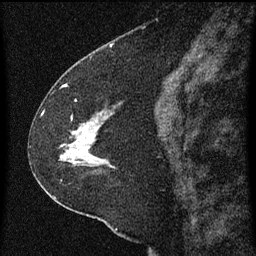
Breast MRI (dynamic contrast-enhanced), one sagittal slice; slice 31 of 60 in the series (ordered by position); dynamic contrast-enhanced series, image 2 of 3 at this slice position (ordered by acquisition); 1.5 T; TE 4.2 ms, TR 8 ms; 256 × 256 image matrix. Patient: female, 47 years.
Annotated regions visible in this slice (semi-automatic segmentation, software-assisted and operator-edited):
- analysis volume of interest (the breast-tissue region the enhancement analysis was run in; not a lesion): box from (x=36, y=96) to (x=117, y=213) px
- tumour enhancement mask (voxels above the 70 % enhancement threshold inside the analysis volume of interest): (x=60, y=118)–(x=105, y=163)